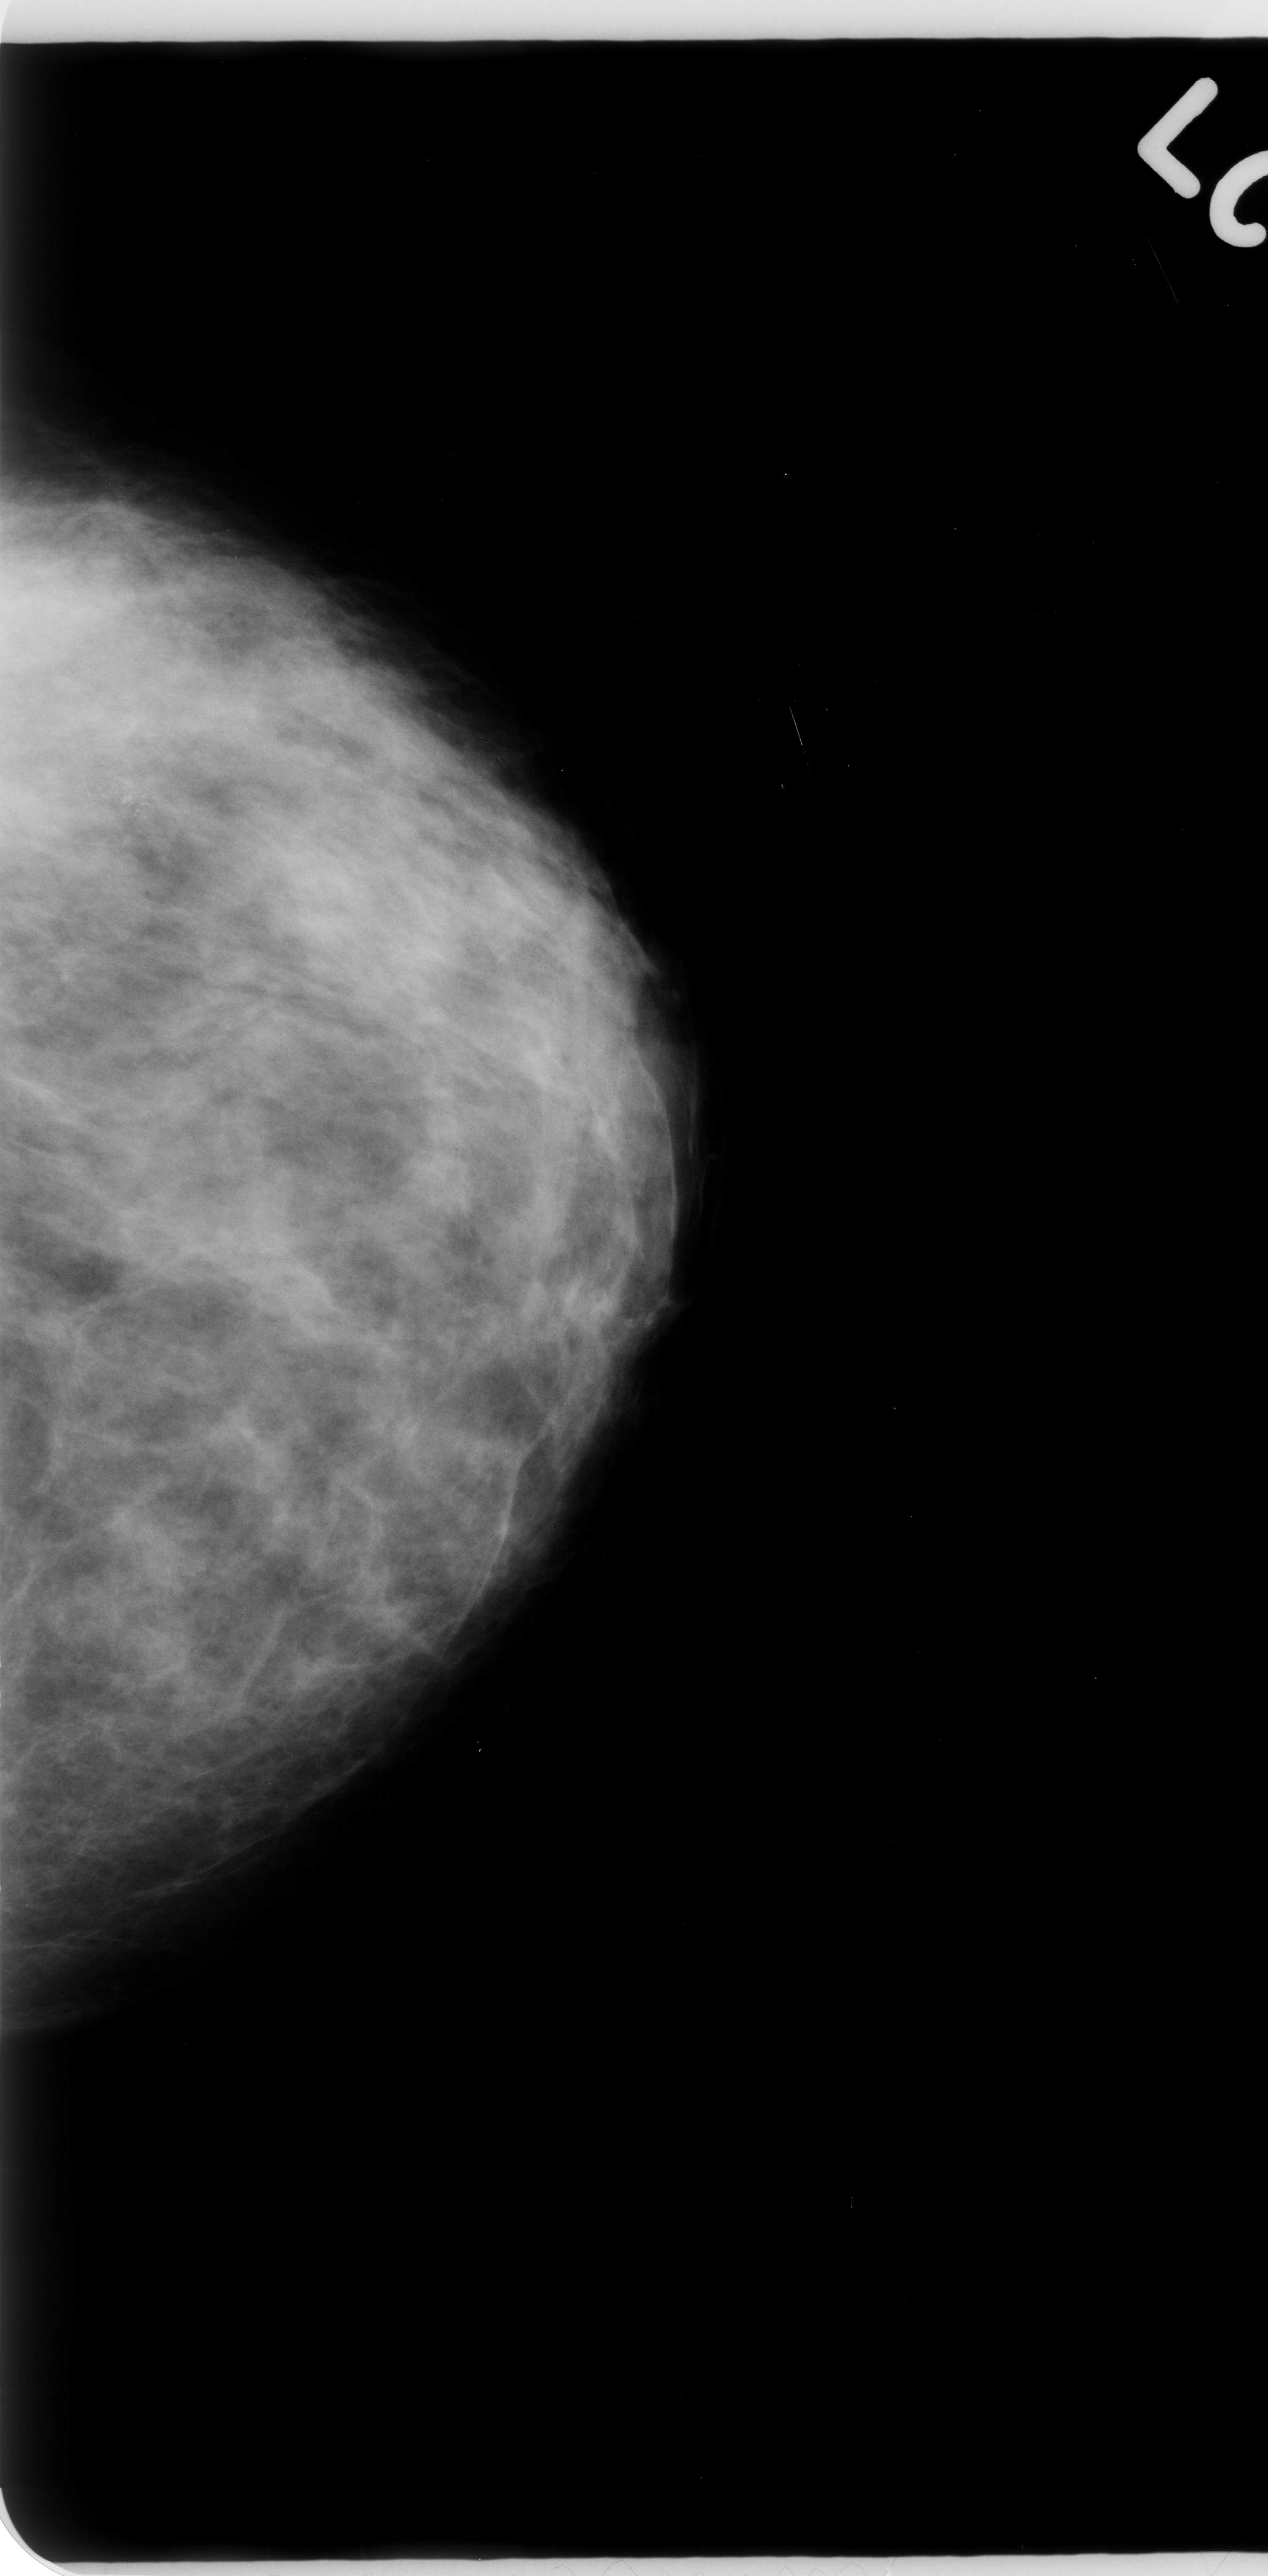
Mammogram (digitized film), left breast, craniocaudal (CC) view, BI-RADS breast density category 2 (scale 1–4).
- Marked abnormality: calcifications, morphology pleomorphic, distribution clustered; BI-RADS assessment category 5; subtlety rating 4 on a 1 (subtle) to 5 (obvious) scale; pathology result (as recorded, not read from the image): malignant.